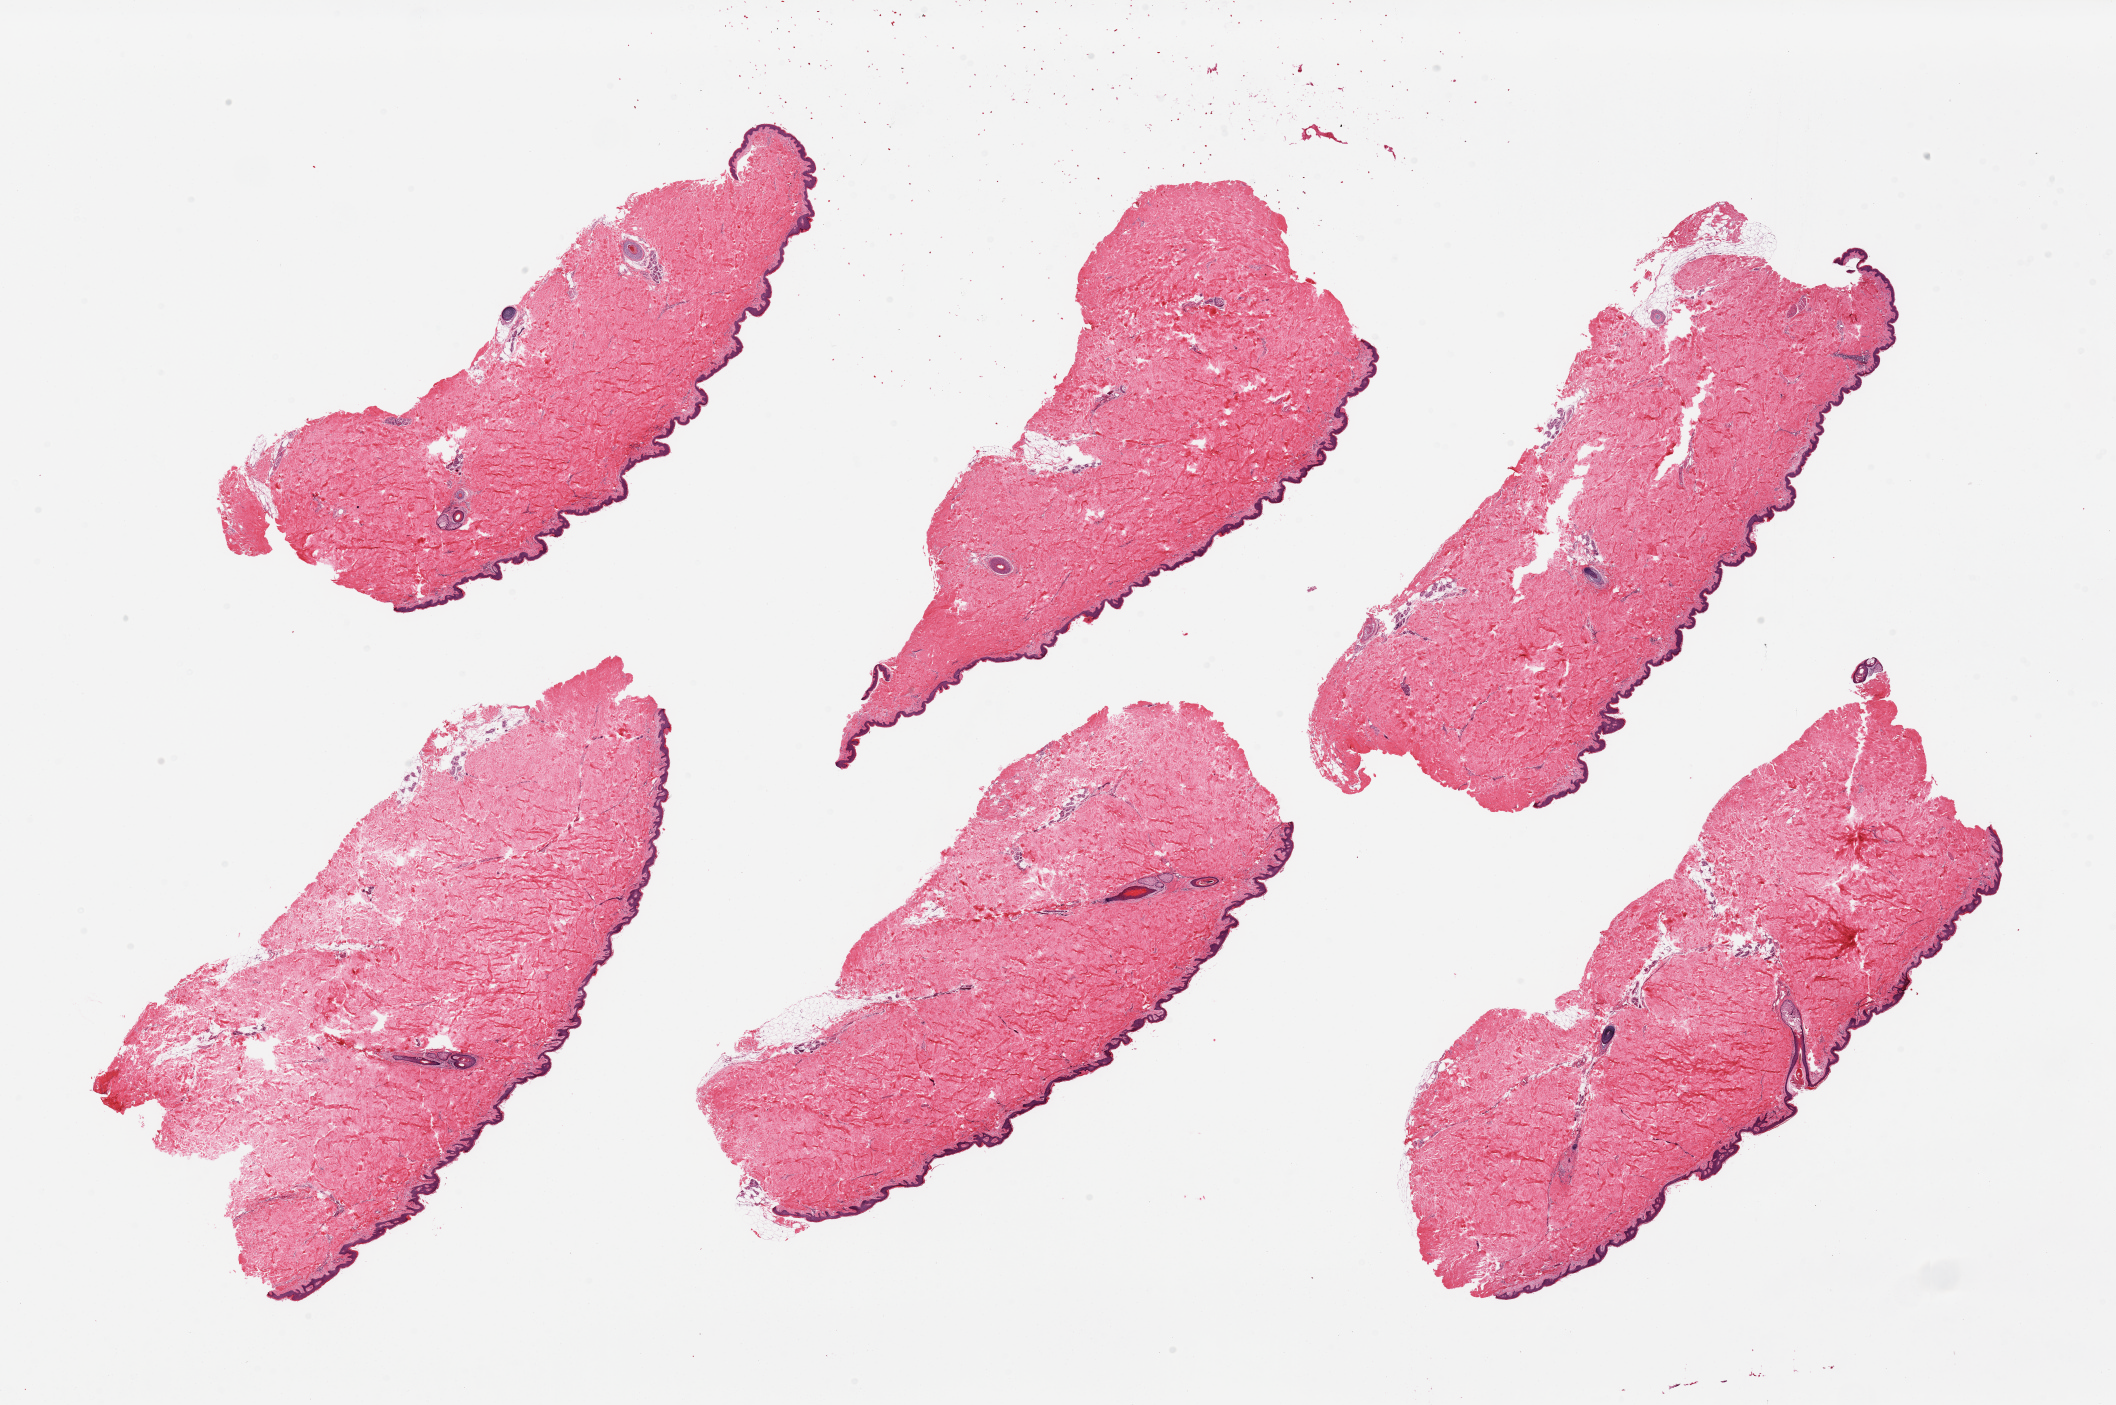
Whole-slide image, hematoxylin and eosin (H&E) stain, brightfield — low-resolution overview of the scanned area, about 33.5 x 22.2 mm, PAXgene-fixed paraffin-embedded (PFPE) section, sampled site (target tissue): skin of suprapubic region, donor tissue sample. Male donor.
Pathologist's review note for this sample: 6 pieces, well trimmed with minimal fat.